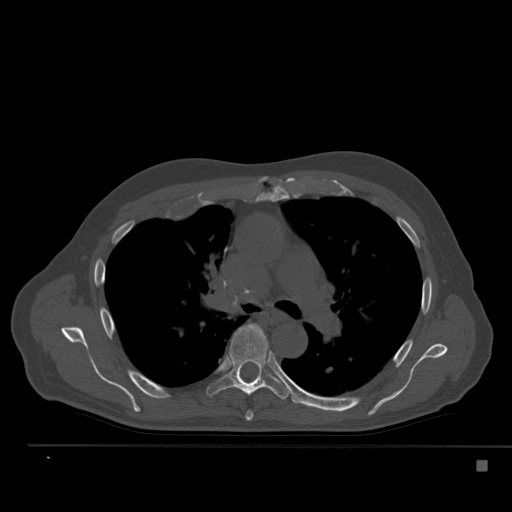
CT including the spine, one axial slice; position 351 of 517 along the scan axis; reconstruction kernel Br40s; 120 kVp; bone window (W 1800 / L 400 HU); 1.5 mm slice thickness; 512 × 512 image matrix, field of view 408 × 408 mm. Patient: male, 70 years. From the clinical record (not read from this slice): primary cancer: renal; vertebrae with lytic lesions (as recorded): T4, T6, T10, T12, L3, L4, L5.
Structures marked on this image (semi-automatic segmentation, software-assisted and operator-edited):
- T5 vertebra: bounding box <245,411,253,421> (left, top, right, bottom; pixels)
- T6 vertebra: <206,324,291,400>